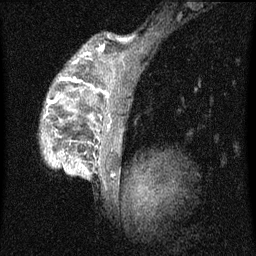
Breast MRI (dynamic contrast-enhanced), one sagittal slice; slice 51 of 60 in the series (ordered by position); dynamic contrast-enhanced series, image 2 of 4 at this slice position (ordered by acquisition); 1.5 T; TE 4.2 ms, TR 8 ms; 2 mm slice thickness; 256 × 256 image matrix, field of view 180 × 180 mm. Patient: female, 50 years.
Structures marked on this image (semi-automatically segmented with operator editing):
- analysis volume of interest (the breast-tissue region the enhancement analysis was run in; not a lesion): bounding box (x1, y1, x2, y2) in pixels: (42, 46, 124, 177)
- tumour enhancement mask (voxels above the 70 % enhancement threshold inside the analysis volume of interest): (48, 80, 109, 169)